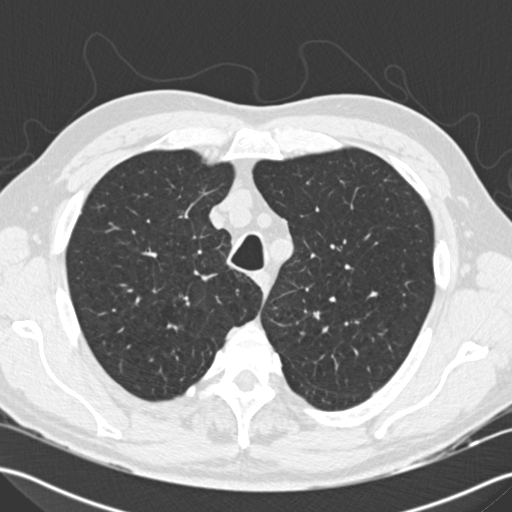
Axial slice from a low-dose chest CT screening exam, first (baseline) screen, lung window (W 1500 / L -600 HU), 2 mm slice thickness, standard (soft-tissue) reconstruction kernel (B30f), slice 43 of 197 in the series. Male participant, aged 66 years at enrolment. Current smoker at enrolment.
• Expert reader's lesion annotation, bounding box <291,299,336,339> (left, top, right, bottom; pixels).
• Screening reader's record for this exam: no non-calcified nodule ≥4 mm recorded.
• Official screen result: negative screen, minor abnormalities not suspicious for lung cancer.
• Later outcome: lung cancer diagnosed 679 days after this screen (after the third annual screen) — squamous cell carcinoma, NOS, left upper lobe, poorly differentiated (G3), stage IA (AJCC 6th edition), 15 mm at pathology.